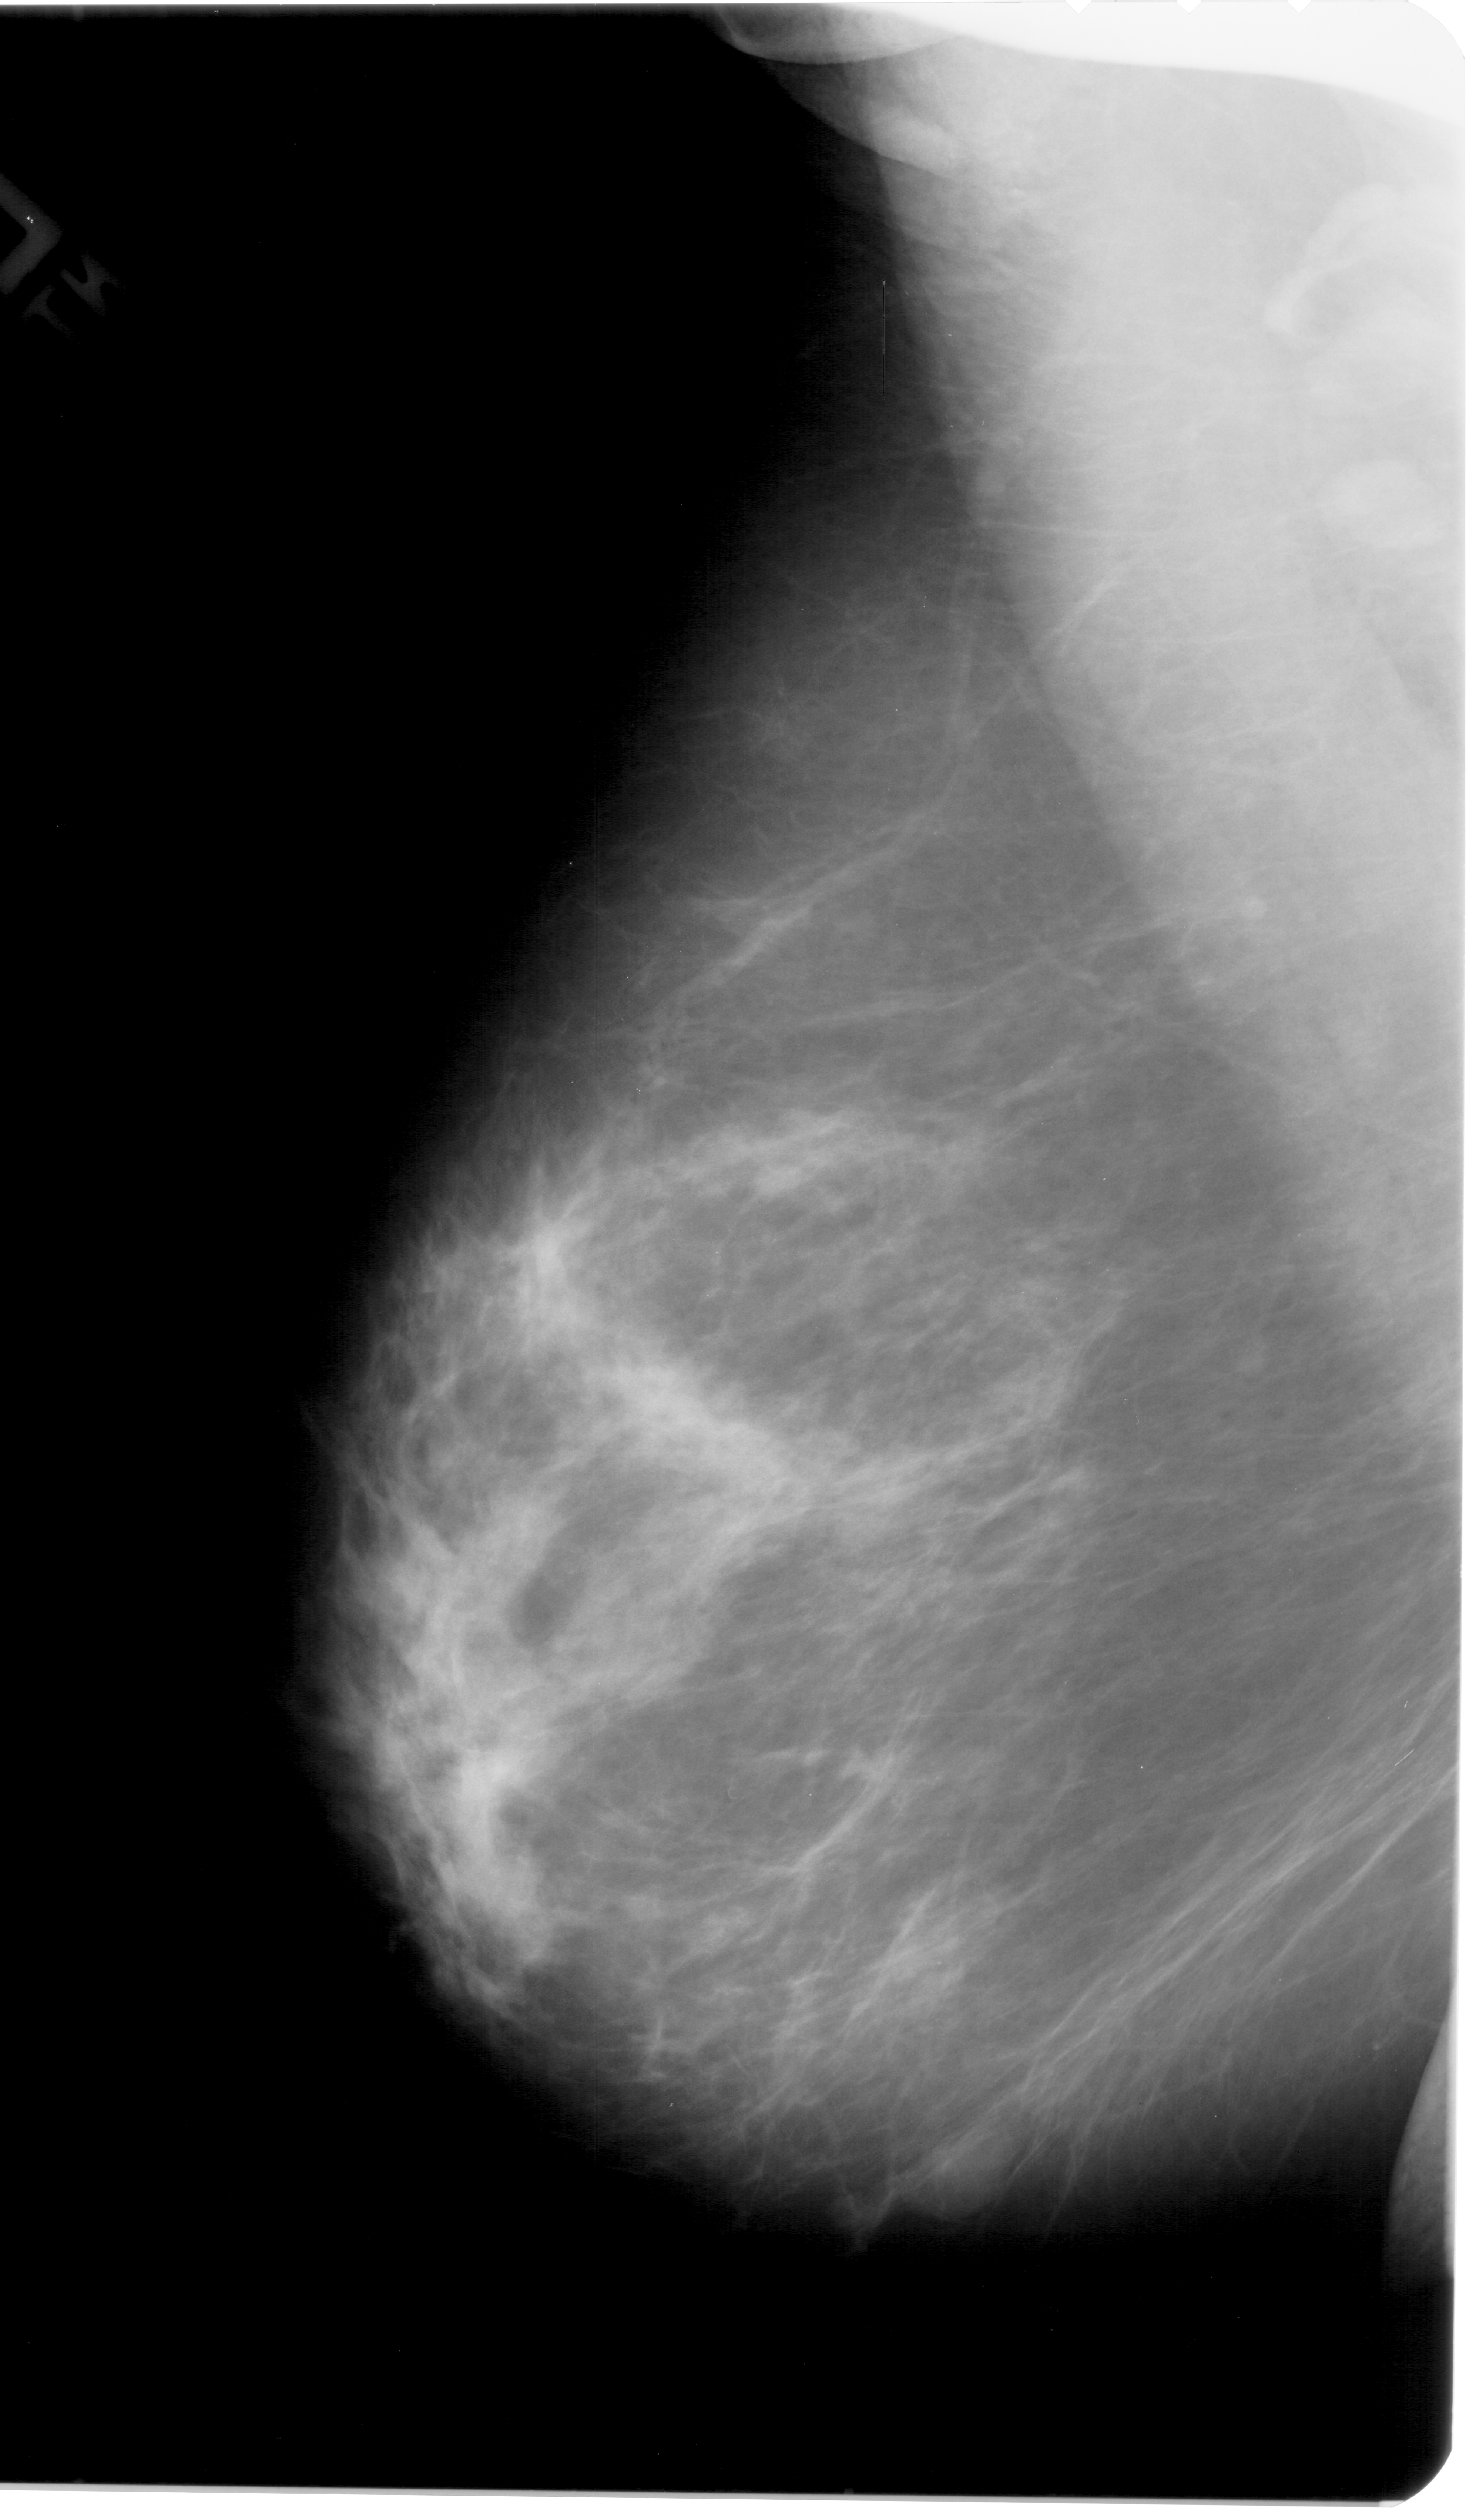
Scanned film-screen mammogram. Left breast. Mediolateral oblique (MLO) view. 1466 × 2520 image matrix.
Expert-marked regions of interest on this film, with their recorded descriptors:
- mass, shape lobulated, margins obscured; BI-RADS assessment category 4; pathology (as recorded): benign: bounding box [x1, y1, x2, y2] px = [907, 2126, 991, 2206]